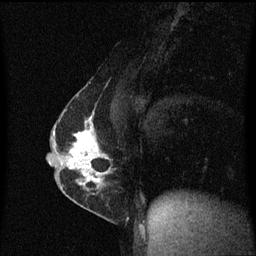
Breast MRI (dynamic contrast-enhanced), one sagittal slice; slice 33 of 60 in the series (ordered by position); dynamic contrast-enhanced series, image 2 of 3 at this slice position (ordered by acquisition); 1.5 T; TE 4.2 ms, TR 8.4 ms; 2 mm slice thickness; 256 × 256 image matrix, field of view 200 × 200 mm. Female patient, age 40 years.
Outlined on this slice (semi-automatically segmented with operator editing):
- analysis volume of interest (the breast-tissue region the enhancement analysis was run in; not a lesion): box from (x=57, y=110) to (x=113, y=191) px
- tumour enhancement mask (voxels above the 70 % enhancement threshold inside the analysis volume of interest): (x=67, y=114)–(x=109, y=189)